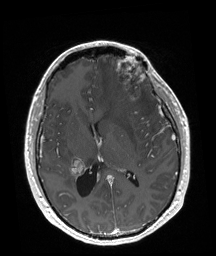
Brain MRI from a brain-tumour surgery series, one axial slice; slice 89 of 192 in the series (ordered by position); T1-weighted post-contrast; 216 × 256 image matrix, field of view 219 × 260 mm.
Structures marked on this image (outlined manually by an expert reader):
- tumour: bounding box [x1, y1, x2, y2] px = [115, 56, 146, 100]